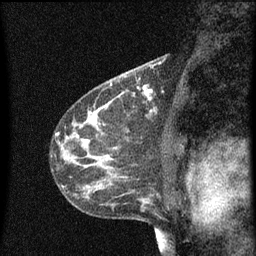
Breast MRI (dynamic contrast-enhanced), one sagittal slice. Position 34 of 60 along the scan axis. Dynamic contrast-enhanced series, image 2 of 3 at this slice position (ordered by acquisition). 1.5 T. TE 4.2 ms, TR 8 ms. 2 mm slice thickness. 256 × 256 image matrix. Female patient, age 41 years.
Annotated regions visible in this slice (semi-automatically segmented with operator editing):
- analysis volume of interest (the breast-tissue region the enhancement analysis was run in; not a lesion): bounding box (x1, y1, x2, y2) in pixels: (130, 76, 155, 101)
- tumour enhancement mask (voxels above the 70 % enhancement threshold inside the analysis volume of interest): (138, 78, 153, 101)